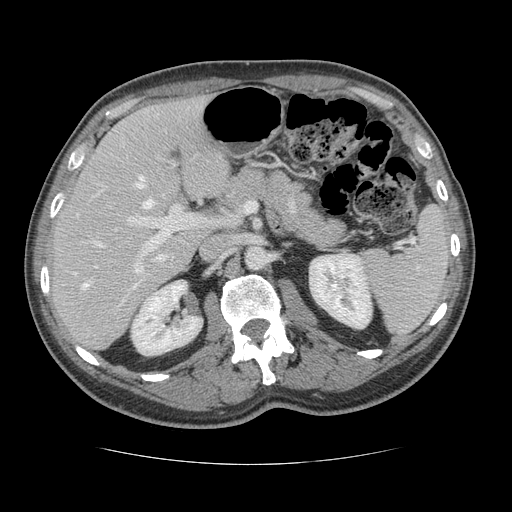
Contrast-enhanced abdominal CT, one axial slice; slice 76 of 134 in the series (ordered by position); reconstruction kernel STANDARD; 120 kVp; intravenous contrast given; soft-tissue window (W 400 / L 40 HU); 2.5 mm slice thickness; 512 × 512 image matrix, field of view 377 × 377 mm. Male patient, age 68 years. Case-level facts recorded for this patient, not image findings: diagnosis: colorectal cancer liver metastases, imaged before liver resection; multiple liver metastases: yes; largest metastasis: 2.2 cm; disease in both lobes: no.
Annotated regions visible in this slice (outlined manually by an expert reader):
- hepatic veins: bounding box <74,175,153,289> (left, top, right, bottom; pixels)
- liver: <51,98,230,350>
- planned liver remnant (the part of the liver to remain after resection): <51,98,230,337>
- portal vein (with intrahepatic branches): <127,164,196,287>